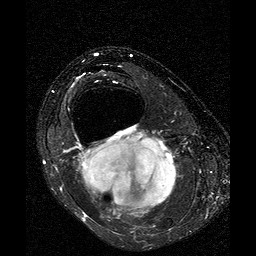
MRI of an extremity soft-tissue mass, one axial slice. Position 21 of 25 along the scan axis. T2-weighted fat-saturated. 256 × 256 image matrix, field of view 160 × 160 mm. Female patient. Case-level facts recorded for this patient, not image findings: histological type: liposarcoma; site of the primary tumour: right thigh.
Outlined on this slice (expert manual segmentation):
- gross tumour volume (mass): bounding box (x1, y1, x2, y2) in pixels: (75, 132, 177, 220)